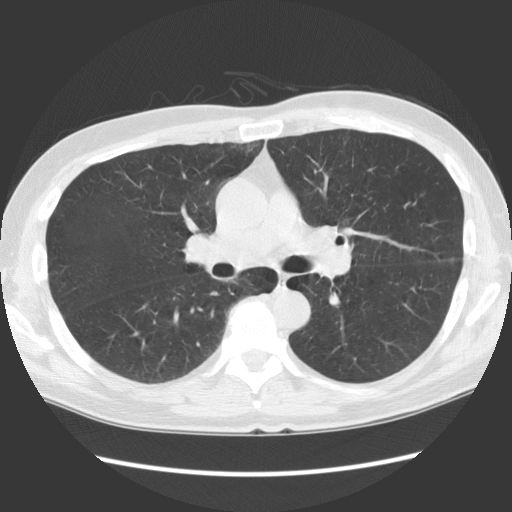
Low-dose screening chest CT, one axial slice. Slice 77 of 136 in the series (ordered by position). 140 kVp. Lung window (W 1500 / L -600 HU). 512 × 512 image matrix, field of view 360 × 360 mm.
Outlined on this slice (expert manual segmentation):
- lesion 1 (tumor, hilum of left lung): bounding box <341,227,353,237> (left, top, right, bottom; pixels)